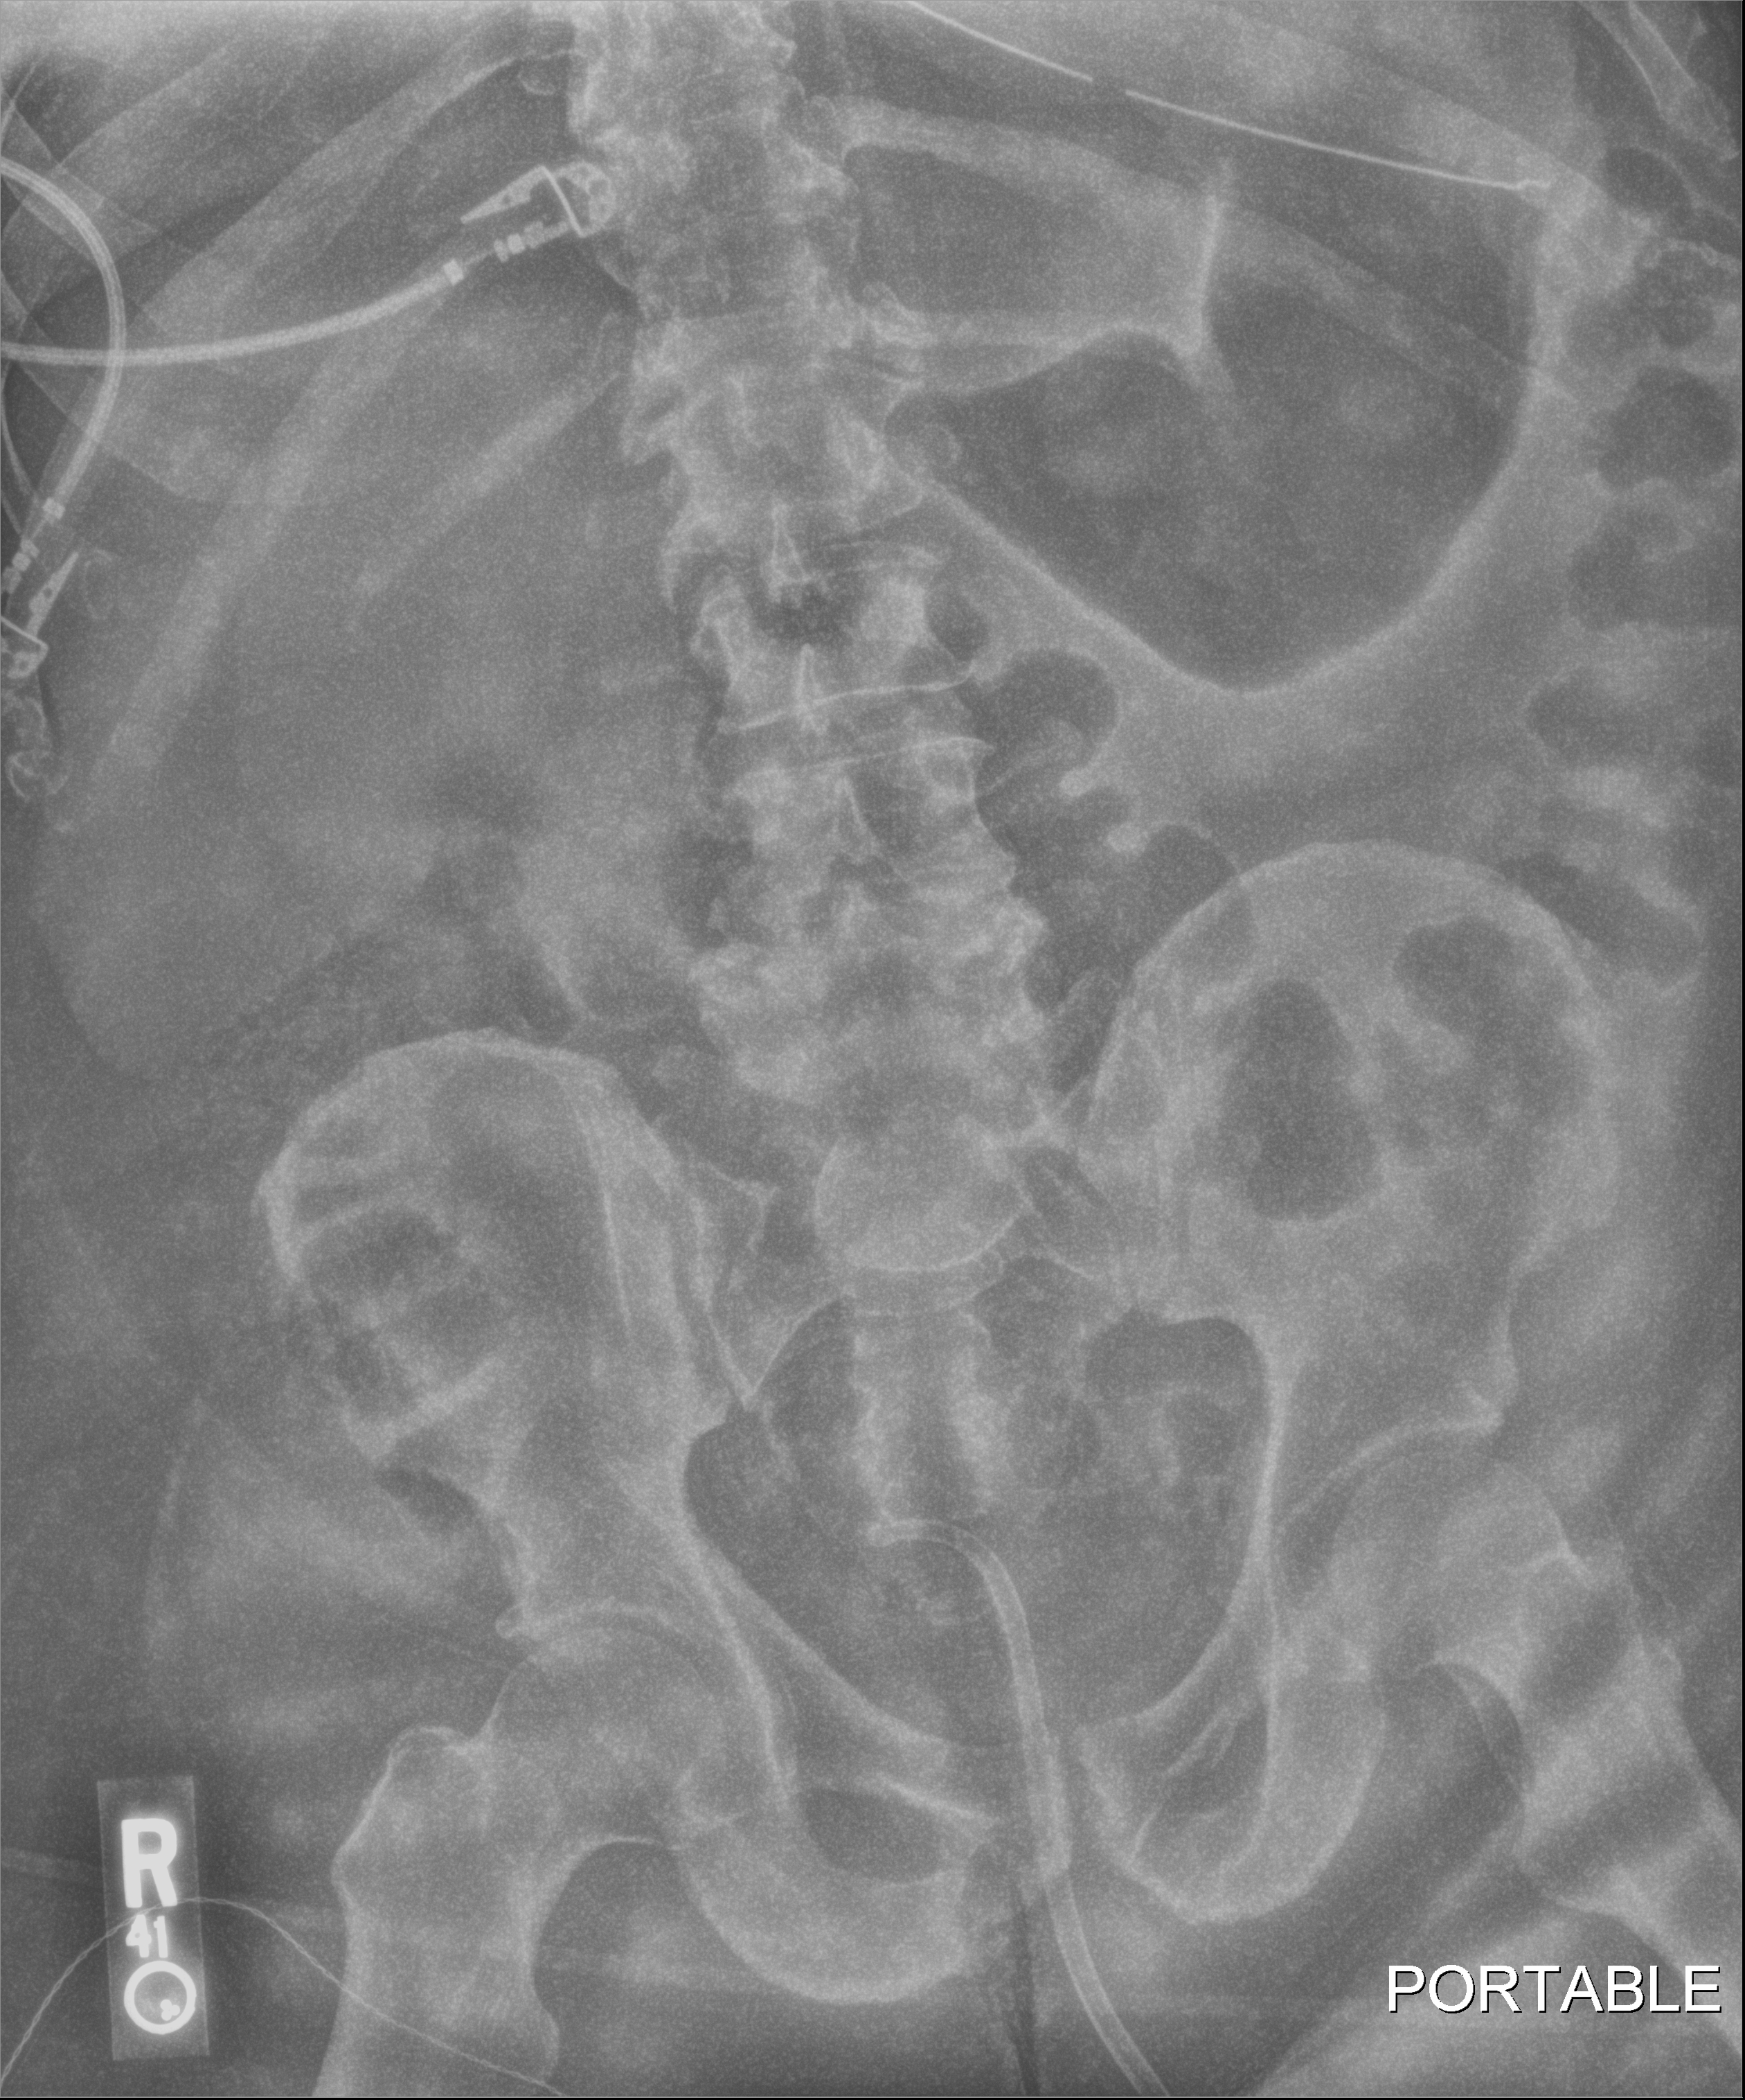
Abdomen X-ray; anteroposterior (AP) projection. Adult patient hospitalised with COVID-19, age 18–59 years.
From the hospital-stay record, not from the radiograph (when in the stay this image was taken is not recorded):
- length of hospital stay: 28 days
- mechanically ventilated during this hospital stay: yes